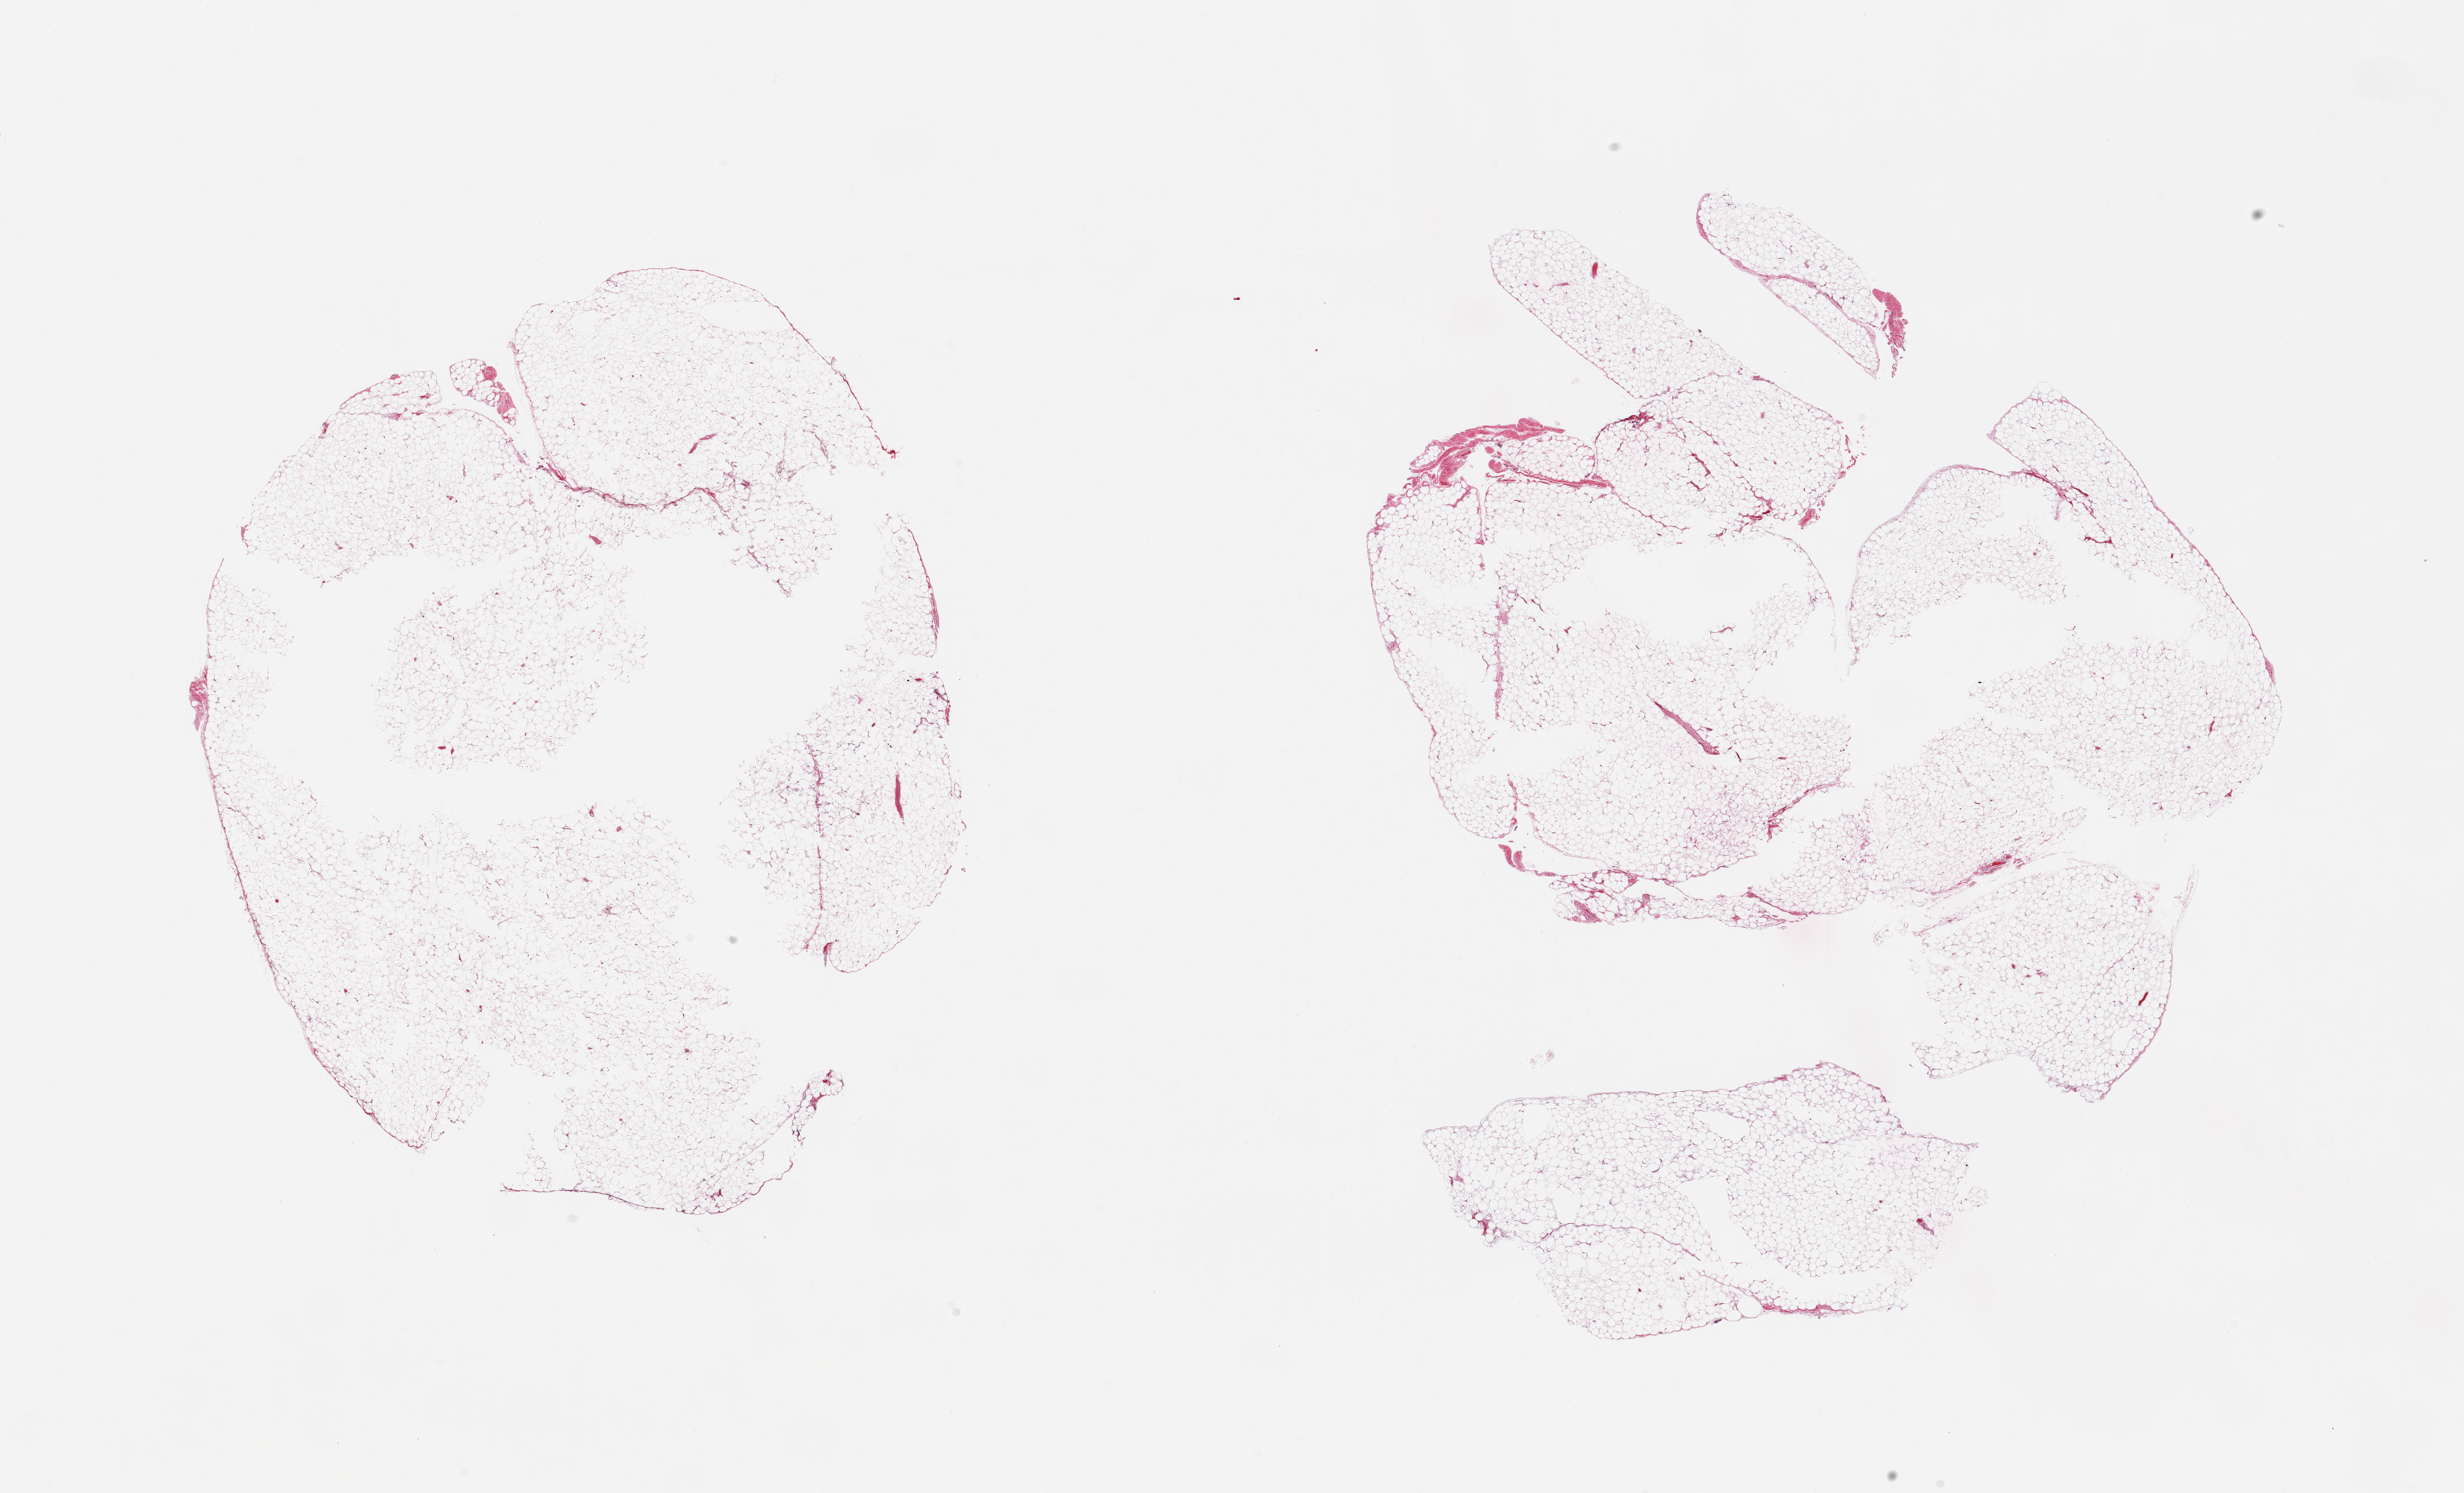
Digitized haematoxylin and eosin-stained section — low-resolution overview of the scanned area, about 26.6 x 16.1 mm (acquisition: 20x scan). PAXgene-fixed paraffin-embedded (PFPE) section. Sampled site (target tissue): omentum. Donor tissue sample.
Reviewer comment on this tissue sample: 2 pieces; mature fat, some central defects.